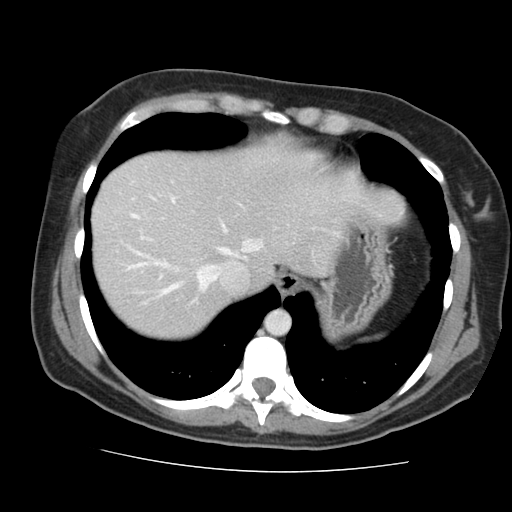
Contrast-enhanced abdominal CT, one axial slice. Slice 127 of 144 in the series (ordered by position). Soft-tissue window (W 400 / L 40 HU). 512 × 512 image matrix, field of view 333 × 333 mm. Female patient, age 46 years. Case-level facts recorded for this patient, not image findings: diagnosis: colorectal cancer liver metastases, imaged before liver resection; multiple liver metastases: no; largest metastasis: 2.8 cm; disease in both lobes: no.
Outlined on this slice (manually delineated by an expert):
- hepatic veins: bounding box [x1, y1, x2, y2] px = [132, 194, 355, 295]
- liver: [93, 142, 343, 338]
- planned liver remnant (the part of the liver to remain after resection): [93, 142, 343, 338]
- portal vein (with intrahepatic branches): [131, 264, 143, 268]